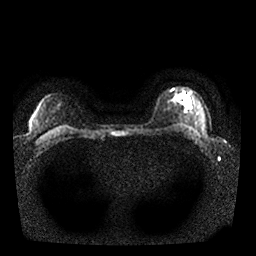
Breast MRI, one axial slice; position 20 of 25 along the scan axis; diffusion-weighted series; image 2 of 4 stored at this slice position (different b-values; order by instance number); 1.5 T; 256 × 256 image matrix, field of view 340 × 340 mm. Female patient.
Annotated regions visible in this slice (outlined manually by an expert reader):
- tumour on diffusion-weighted imaging: bounding box <181,96,190,104> (left, top, right, bottom; pixels)